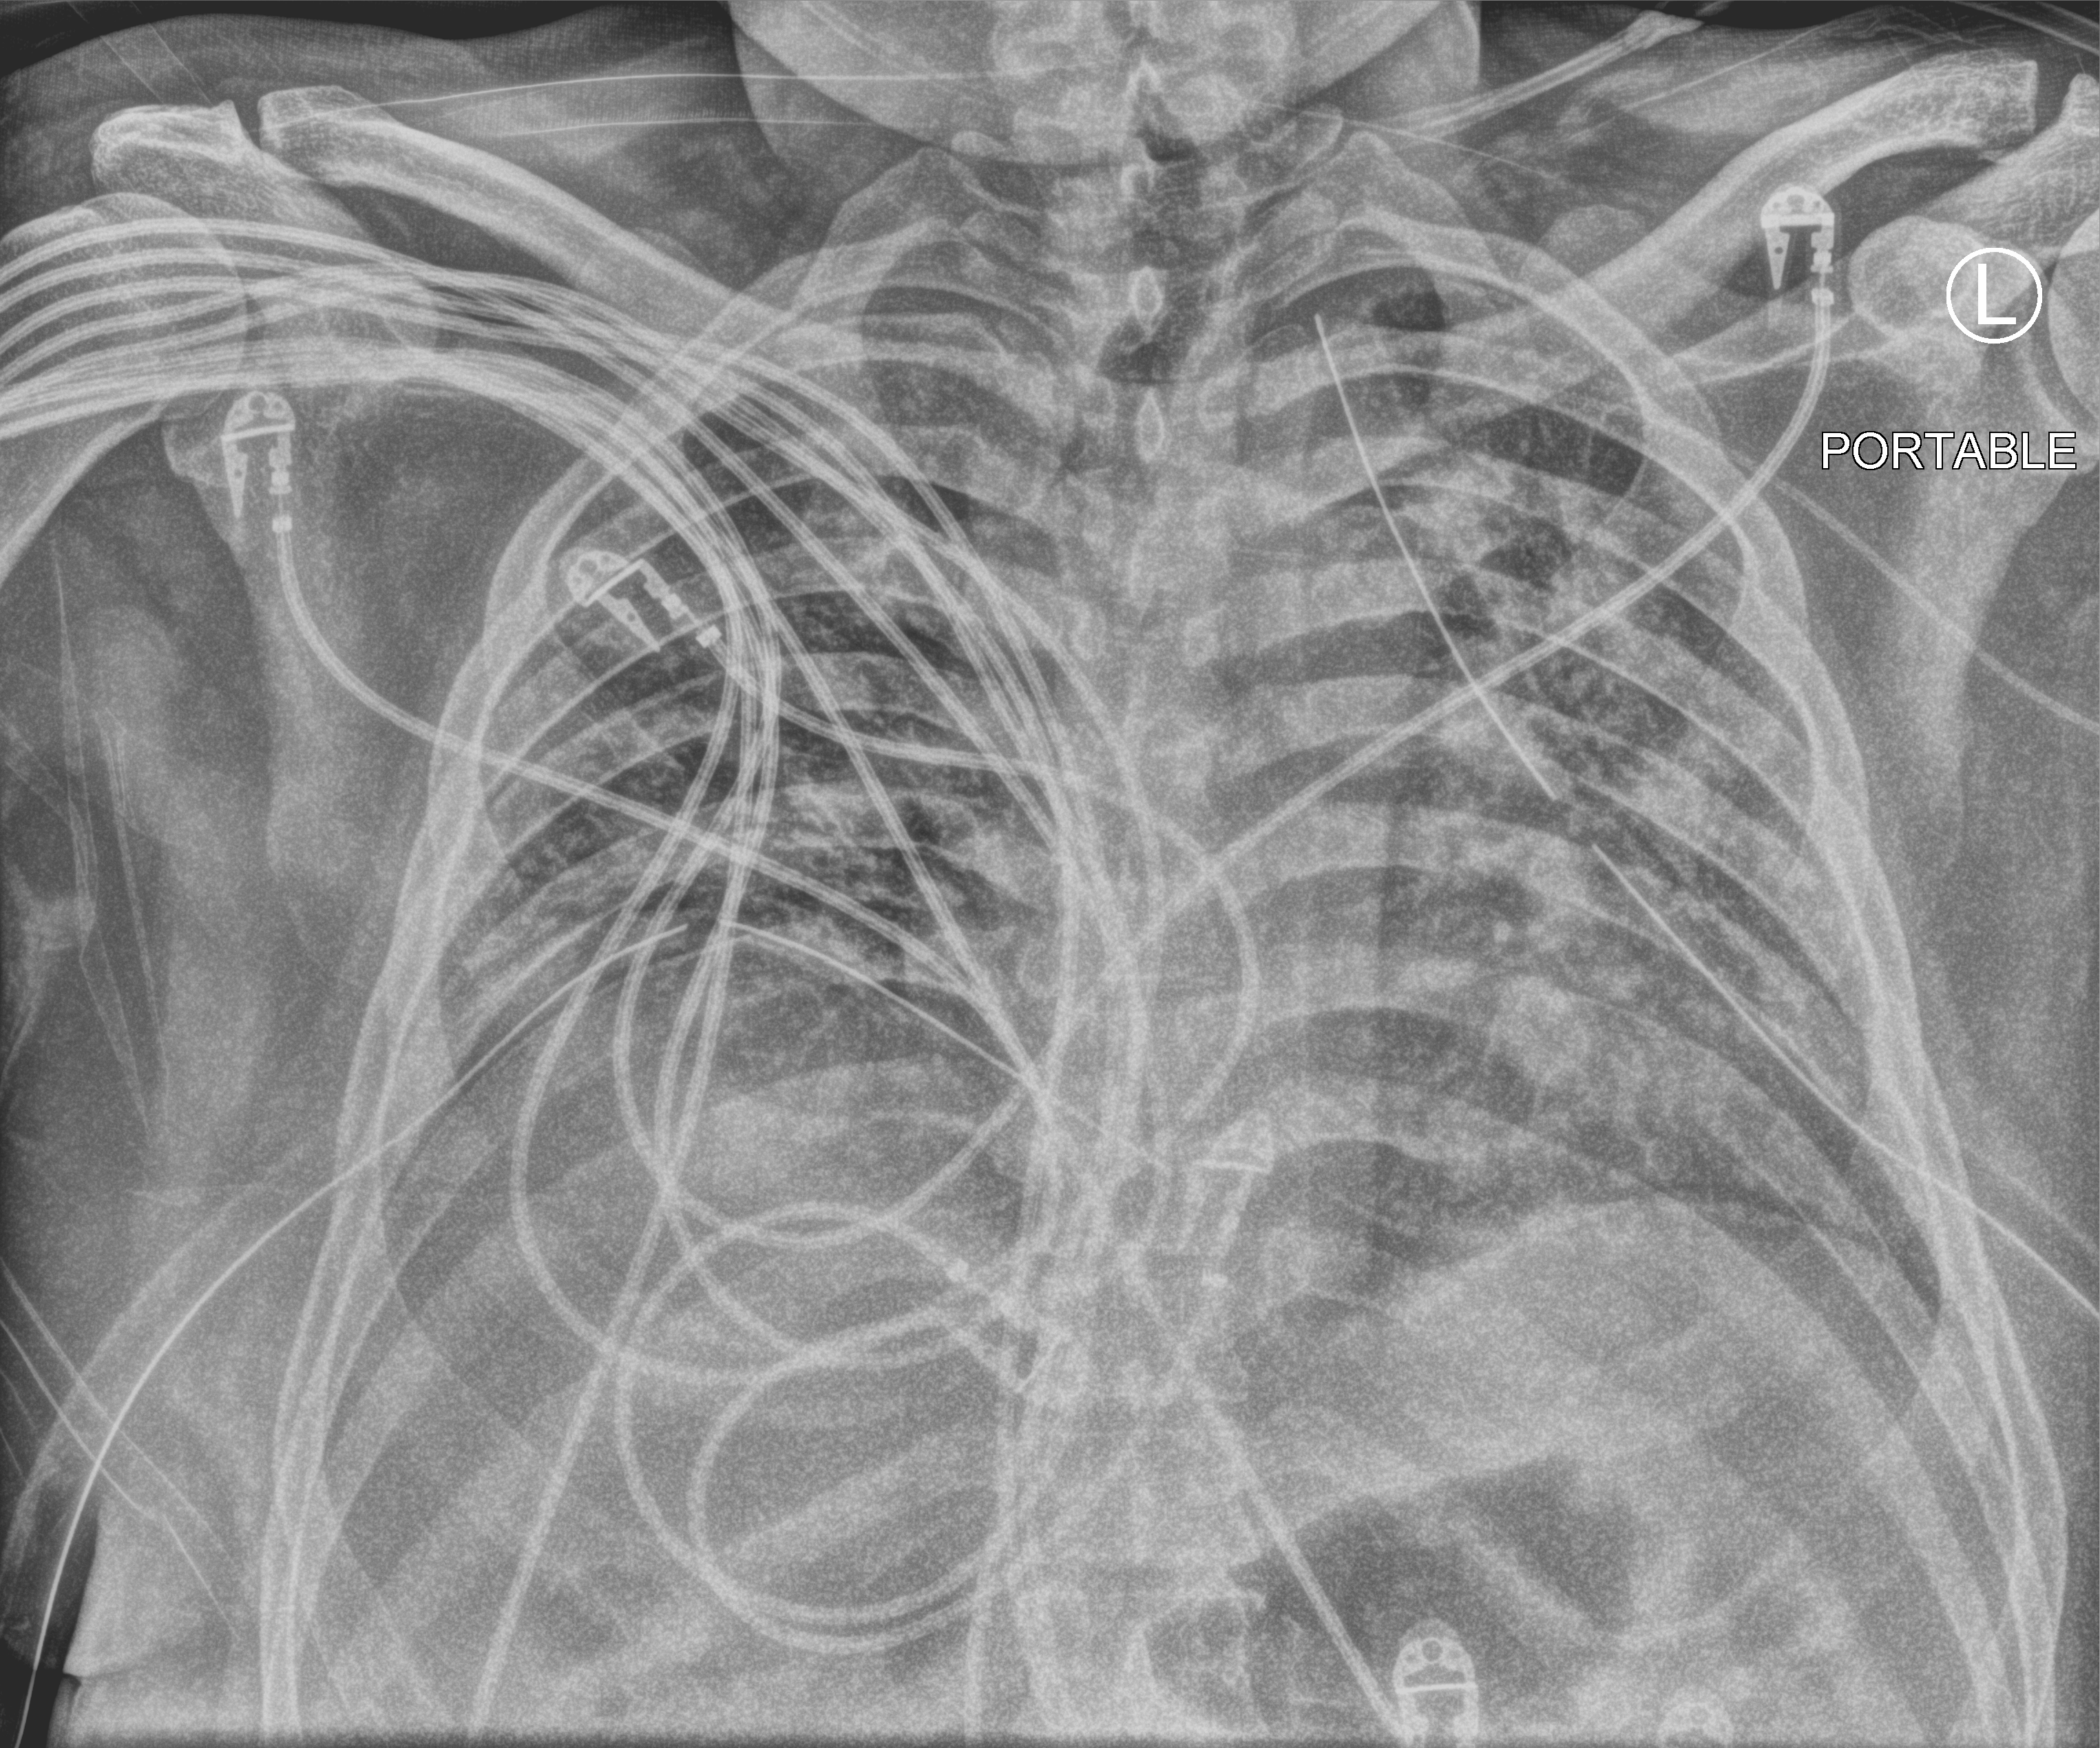
Chest X-ray (portable), anteroposterior (AP) projection. Male patient hospitalised with COVID-19, age 18–59 years.
From the hospital-stay record, not from the radiograph (when in the stay this image was taken is not recorded): mechanically ventilated during this hospital stay: yes.